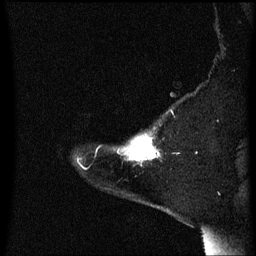
Breast MRI (dynamic contrast-enhanced), one sagittal slice. Position 52 of 60 along the scan axis. Dynamic contrast-enhanced series, image 2 of 3 at this slice position (ordered by acquisition). 1.5 T. TE 4.2 ms, TR 8.4 ms. 256 × 256 image matrix. Patient: female, 54 years. Case-level facts recorded for this patient, not image findings: setting: breast cancer imaged before/during neoadjuvant chemotherapy; receptor status: HR-positive, HER2-negative.
Structures marked on this image (semi-automatically segmented with operator editing):
- analysis volume of interest (the breast-tissue region the enhancement analysis was run in; not a lesion): box from (x=121, y=134) to (x=161, y=167) px
- tumour enhancement mask (voxels above the 70 % enhancement threshold inside the analysis volume of interest): (x=128, y=134)–(x=160, y=161)